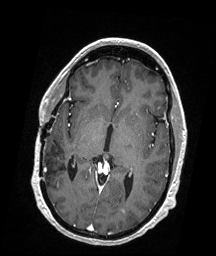
Brain MRI from a brain-tumour surgery series, one axial slice. Slice 96 of 176 in the series (ordered by position). T1-weighted post-contrast. 216 × 256 image matrix. Case-level facts recorded for this patient, not image findings: histopathology: Demyelinating Lesions (Multiple Sclerosis Plaques); tumour location: Left Occipital.
Structures marked on this image (outlined manually by an expert reader):
- tumour: bounding box [x1, y1, x2, y2] px = [121, 208, 127, 214]